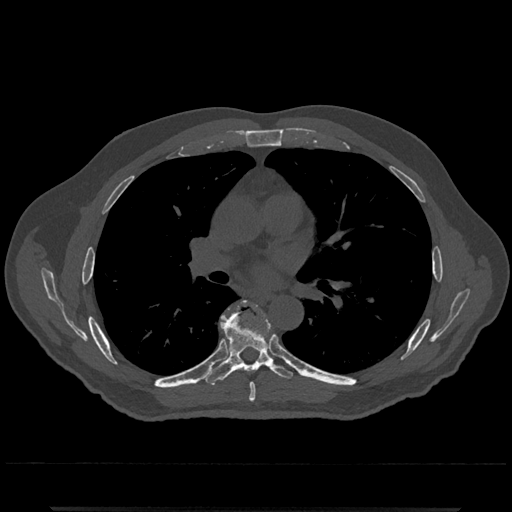
CT including the spine, one axial slice; position 740 of 797 along the scan axis; 120 kVp; bone window (W 1800 / L 400 HU); 0.5 mm slice thickness; 512 × 512 image matrix. Male patient, age 67 years. Case-level facts recorded for this patient, not image findings: primary cancer: prostate.
Annotated regions visible in this slice (semi-automatically segmented with operator editing):
- T6 vertebra: bounding box [x1, y1, x2, y2] px = [249, 383, 256, 402]
- T7 vertebra: [202, 303, 294, 386]